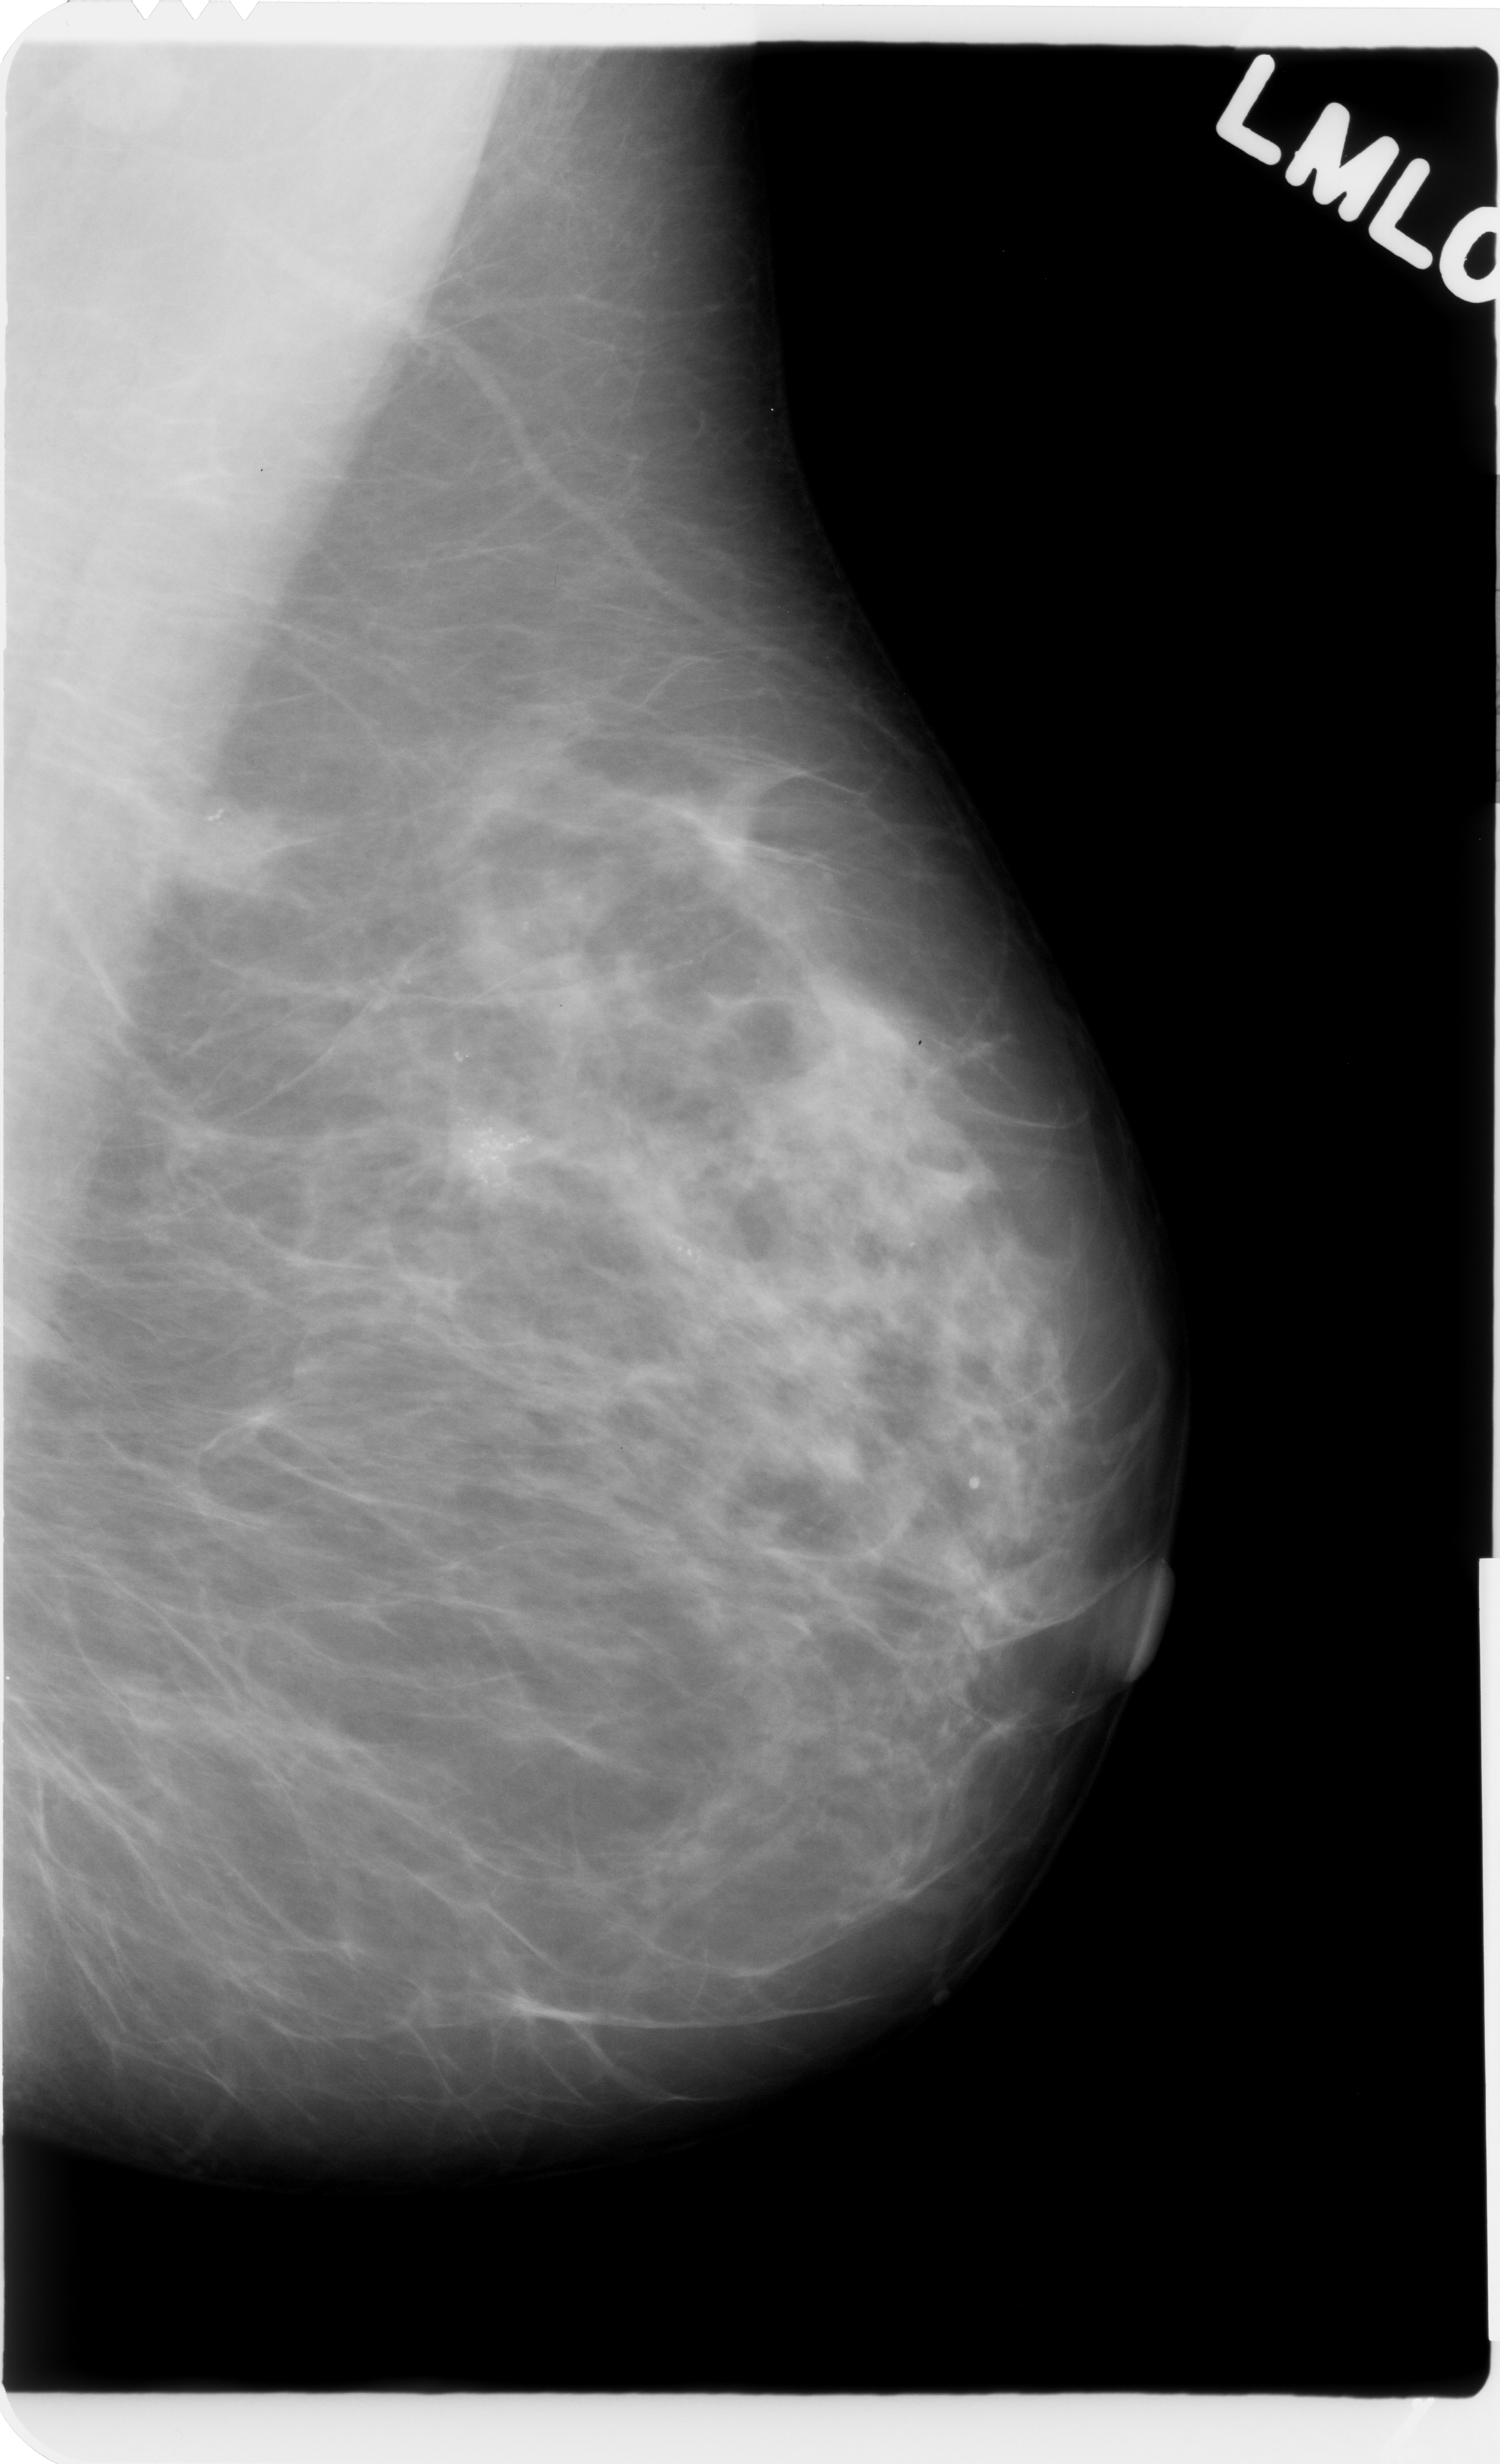
Mammogram (digitized film). Left breast. MLO view. BI-RADS breast density category 2 (scale 1–4). 1500 × 2464 image matrix.
Expert-marked regions of interest on this film, with their recorded descriptors:
- Finding 1 of 3: calcifications, morphology pleomorphic, distribution clustered; BI-RADS assessment category 5; subtlety rating 5 on a 1 (subtle) to 5 (obvious) scale; pathology (as recorded): malignant: bounding box <16,645,397,994> (left, top, right, bottom; pixels)
- Finding 2 of 3: calcifications, morphology pleomorphic, distribution clustered; BI-RADS assessment category 5; pathology result (as recorded, not read from the image): malignant: <318,1046,606,1317>
- Finding 3 of 3: calcifications, morphology pleomorphic, distribution clustered; BI-RADS assessment category 5; pathology result (as recorded, not read from the image): malignant: <592,1115,814,1358>